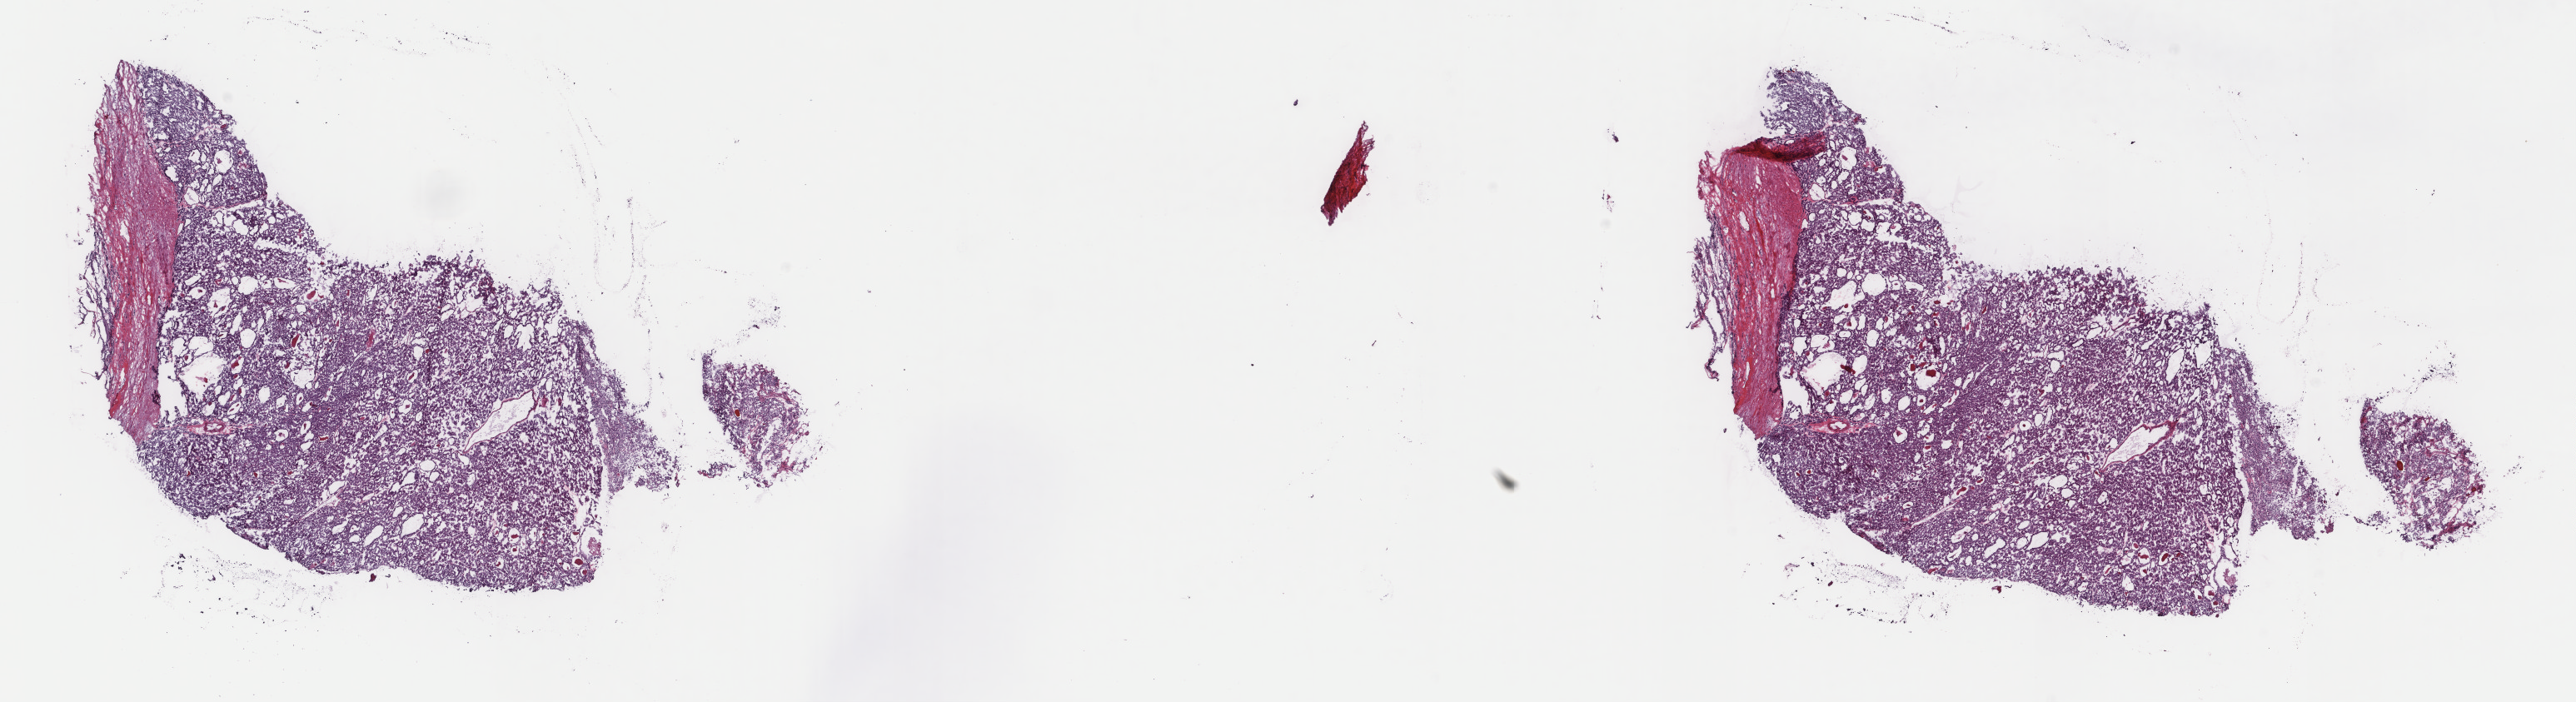
Digitized Hematoxylin and eosin (H&E) stained tissue section (whole slide) — whole scanned area (about 24.6 x 6.7 mm, slide scanned at 40x) shown as a low-resolution overview. Frozen section from the top of the tissue portion. Thyroid, primary tumour sample. Female patient; age at initial diagnosis 33 years. Pathologist review of this section (percent, as recorded): tumour cells 90%, tumour nuclei 100%, normal cells 0%, stromal cells 10%, necrosis 0%. Inflammatory infiltration, as recorded: lymphocyte infiltration 0%, monocyte infiltration 0%, neutrophil infiltration 0%.
* pathologic diagnosis: Papillary carcinoma, follicular variant (thyroid gland)
* AJCC pathologic stage: I (7th edition)
* laterality: right
* TNM: T1b N0 MX